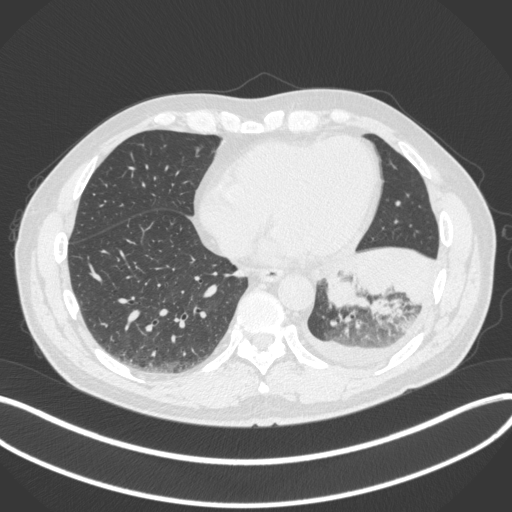
Chest CT, one axial slice. Position 113 of 350 along the scan axis. Reconstruction kernel B31f. Lung window (W 1500 / L -600 HU). 1 mm slice thickness. 512 × 512 image matrix, field of view 400 × 400 mm. Male patient, age 58 years. From the clinical record (not read from this slice): clinical TNM (as recorded): T3 N1 M1b; histopathological grade: G3.
Annotated regions visible in this slice (rectangle marked by the reading radiologist):
- lung tumour (recorded histology: small cell carcinoma): box from (x=317, y=263) to (x=369, y=313) px